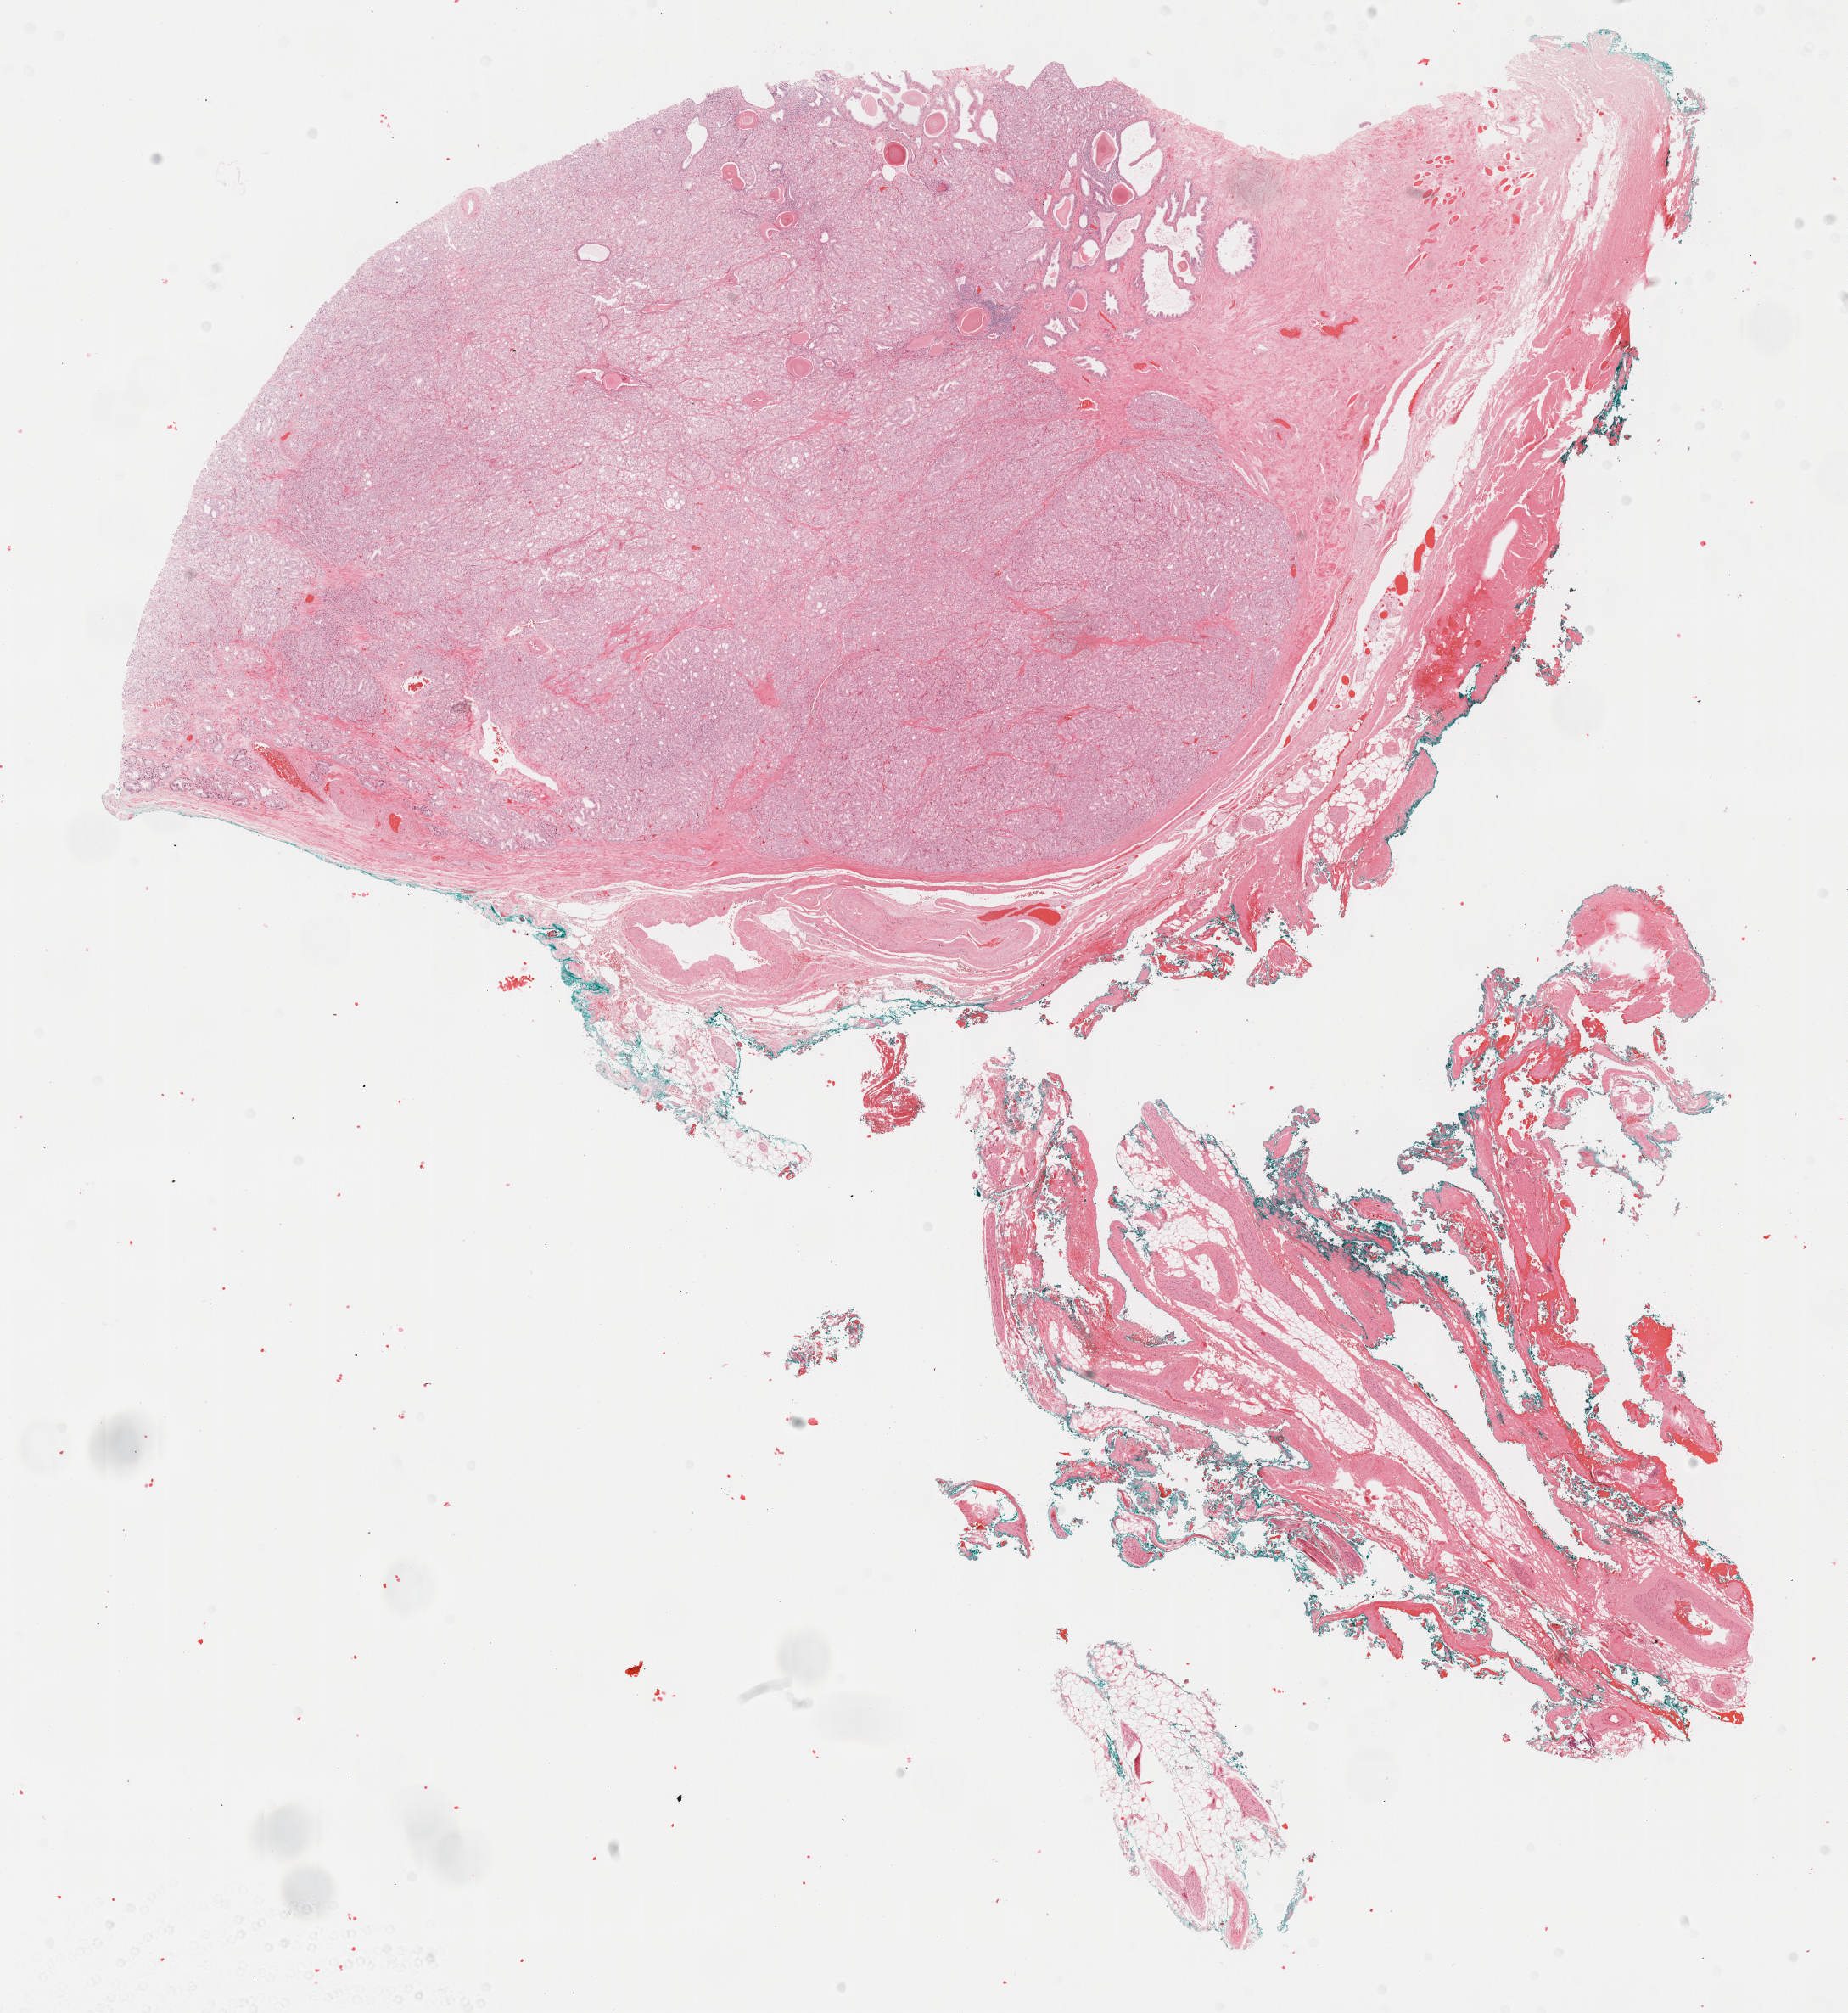
H&E-stained whole-slide image — shown as a low-resolution overview of the whole scanned area (about 17.6 x 19.2 mm, slide scanned at 40x), formalin-fixed paraffin-embedded (FFPE) diagnostic section, sample: primary tumour, prostate. Male, age 72 years at initial diagnosis. Gleason score: 8 (4+4).
Lymph nodes positive (case pathology): 0 of 4 examined. Laterality: bilateral. Diagnosis: Adenocarcinoma, NOS (prostate gland).